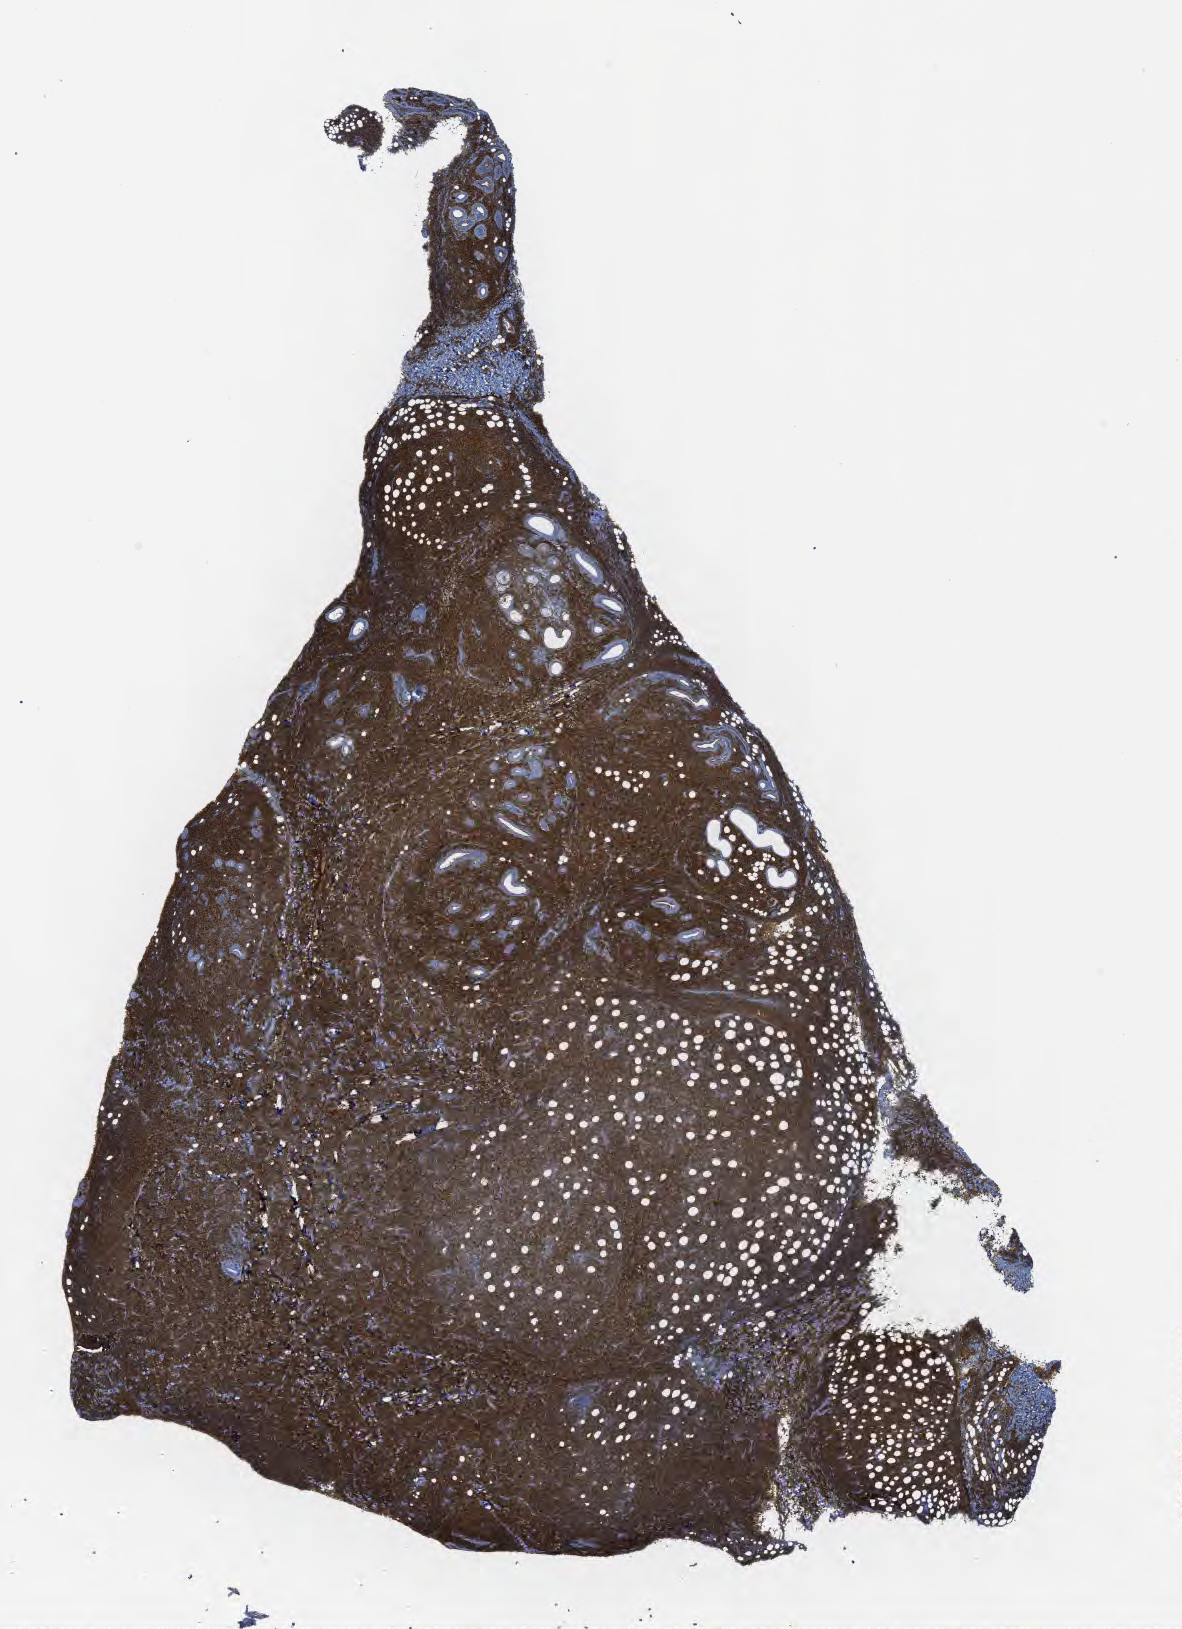
IHC for CD10, whole-slide image, a low-resolution overview of the entire scanned area, about 9.6 x 13.2 mm, tumor tissue. Patient: male, age 46 years.
Histologic diagnosis: Burkitt lymphoma, NOS.